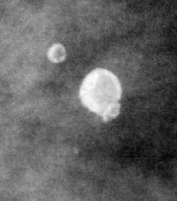
Crop from a digitized film mammogram around one marked abnormality; right breast; MLO view.
- Calcifications, morphology round and regular / eggshell; BI-RADS assessment category 2; subtlety rating 3 on a 1 (subtle) to 5 (obvious) scale; benign without callback (not worked up further).